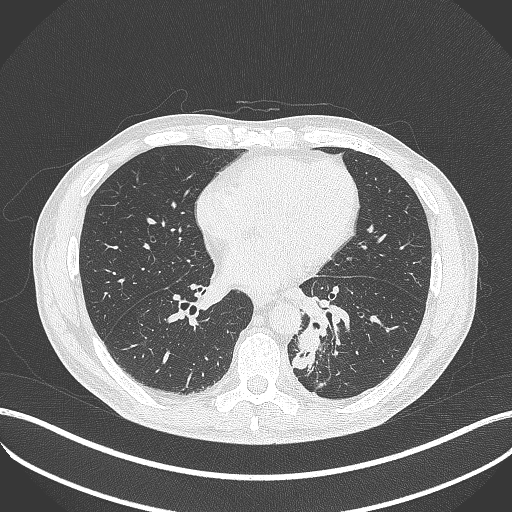
Chest CT, one axial slice; slice 168 of 451 in the series (ordered by position); lung window (W 1500 / L -600 HU); 1 mm slice thickness; 512 × 512 image matrix, field of view 400 × 400 mm. Male patient, age 72 years. Case-level facts recorded for this patient, not image findings: clinical TNM (as recorded): T2b N0 M1.
Annotated regions visible in this slice (rectangle marked by the reading radiologist):
- lung tumour (recorded histology: adenocarcinoma): box from (x=294, y=321) to (x=326, y=374) px